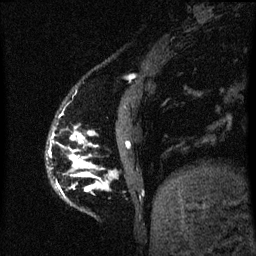
Breast MRI (dynamic contrast-enhanced), one sagittal slice. Position 10 of 60 along the scan axis. Dynamic contrast-enhanced series, image 2 of 3 at this slice position (ordered by acquisition). 1.5 T. TE 4.2 ms, TR 8 ms. 2 mm slice thickness. 256 × 256 image matrix, field of view 190 × 190 mm. Patient: female, 50 years.
Structures marked on this image (semi-automatic segmentation, software-assisted and operator-edited):
- analysis volume of interest (the breast-tissue region the enhancement analysis was run in; not a lesion): box from (x=57, y=136) to (x=91, y=191) px
- tumour enhancement mask (voxels above the 70 % enhancement threshold inside the analysis volume of interest): (x=71, y=136)–(x=90, y=191)